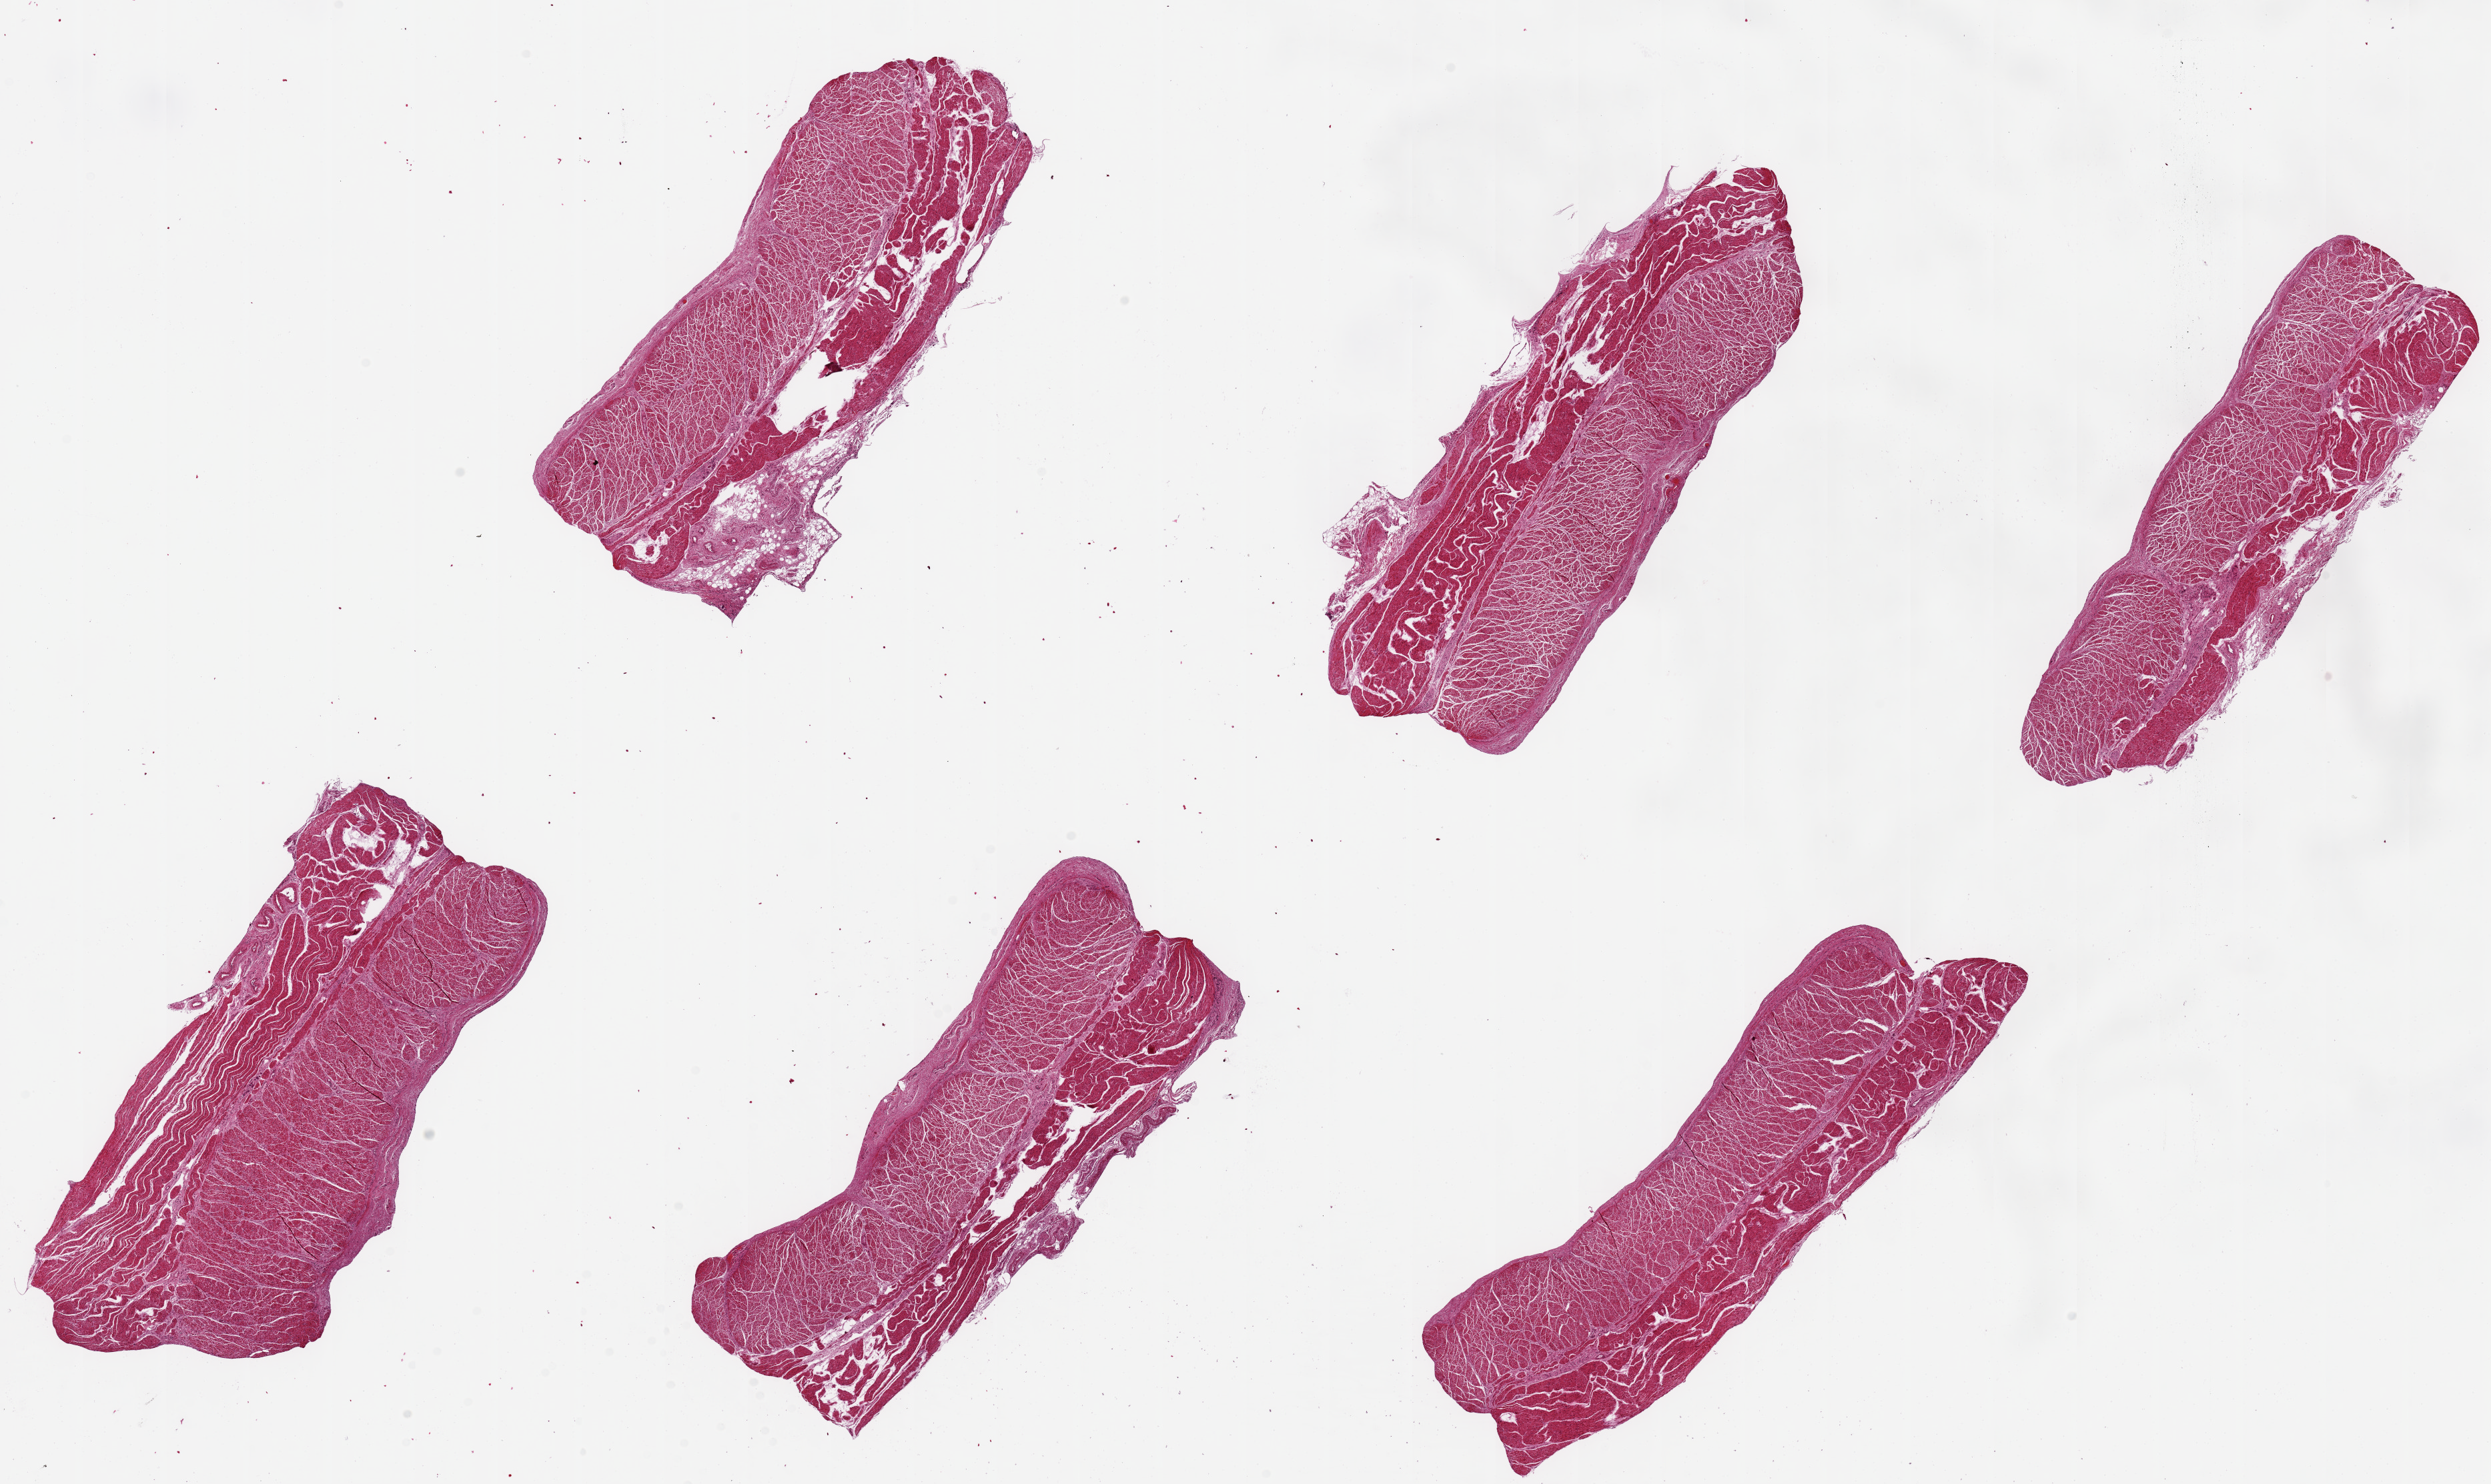
Whole-slide image, H&E stain, a low-resolution overview of the entire scanned area, about 29.5 x 17.6 mm (acquisition: 20x scan); PAXgene-fixed paraffin-embedded (PFPE) section; target tissue: esophageal muscle; tissue donor sample.
Reviewer comment on this tissue sample: 6 pieces, up to 8x2mm; all muscularis.